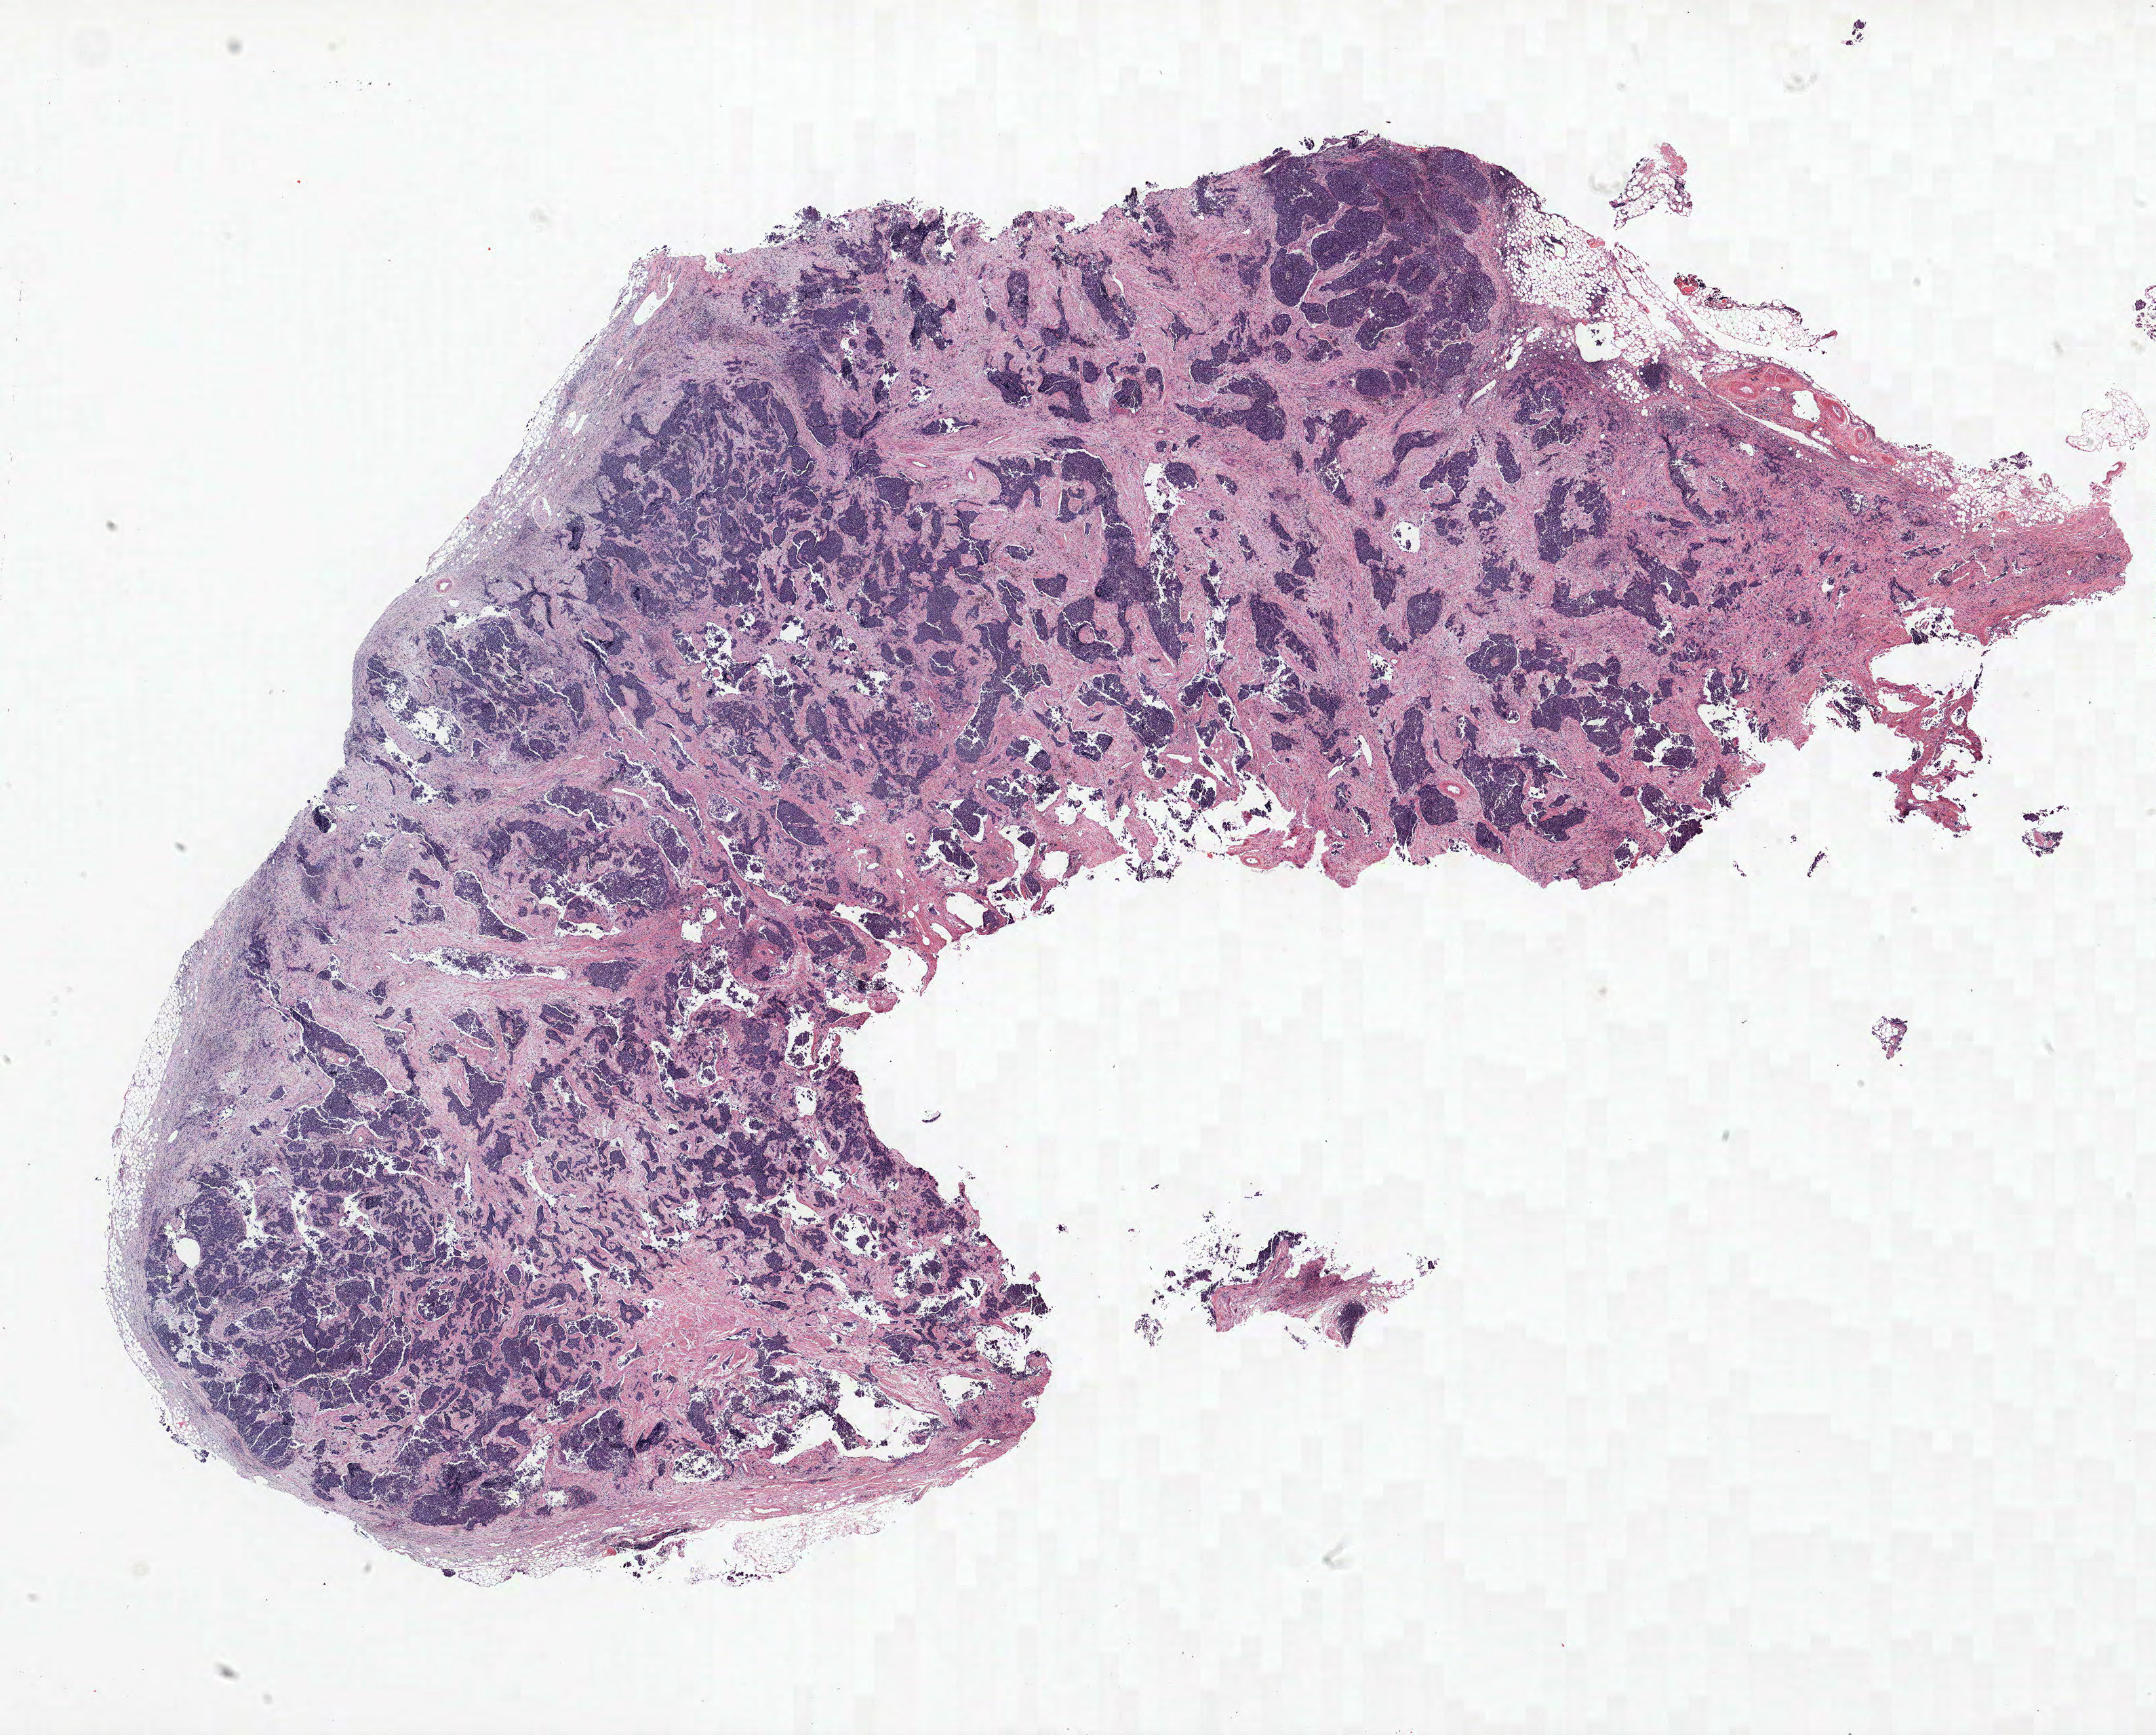
H&E whole-slide image, shown as a low-resolution overview of the whole scanned area (about 25.4 x 20.5 mm); FFPE section; lung tissue. Male, age 73 at enrolment. Current smoker at enrolment. Grade: cannot be assessed (GX).
• primary tumour location (clinical record): left upper lobe
• participant's lung-cancer diagnosis: Small cell carcinoma, NOS
• tumour size (pathology): 19 mm
• stage (AJCC 6th edition): IIIB